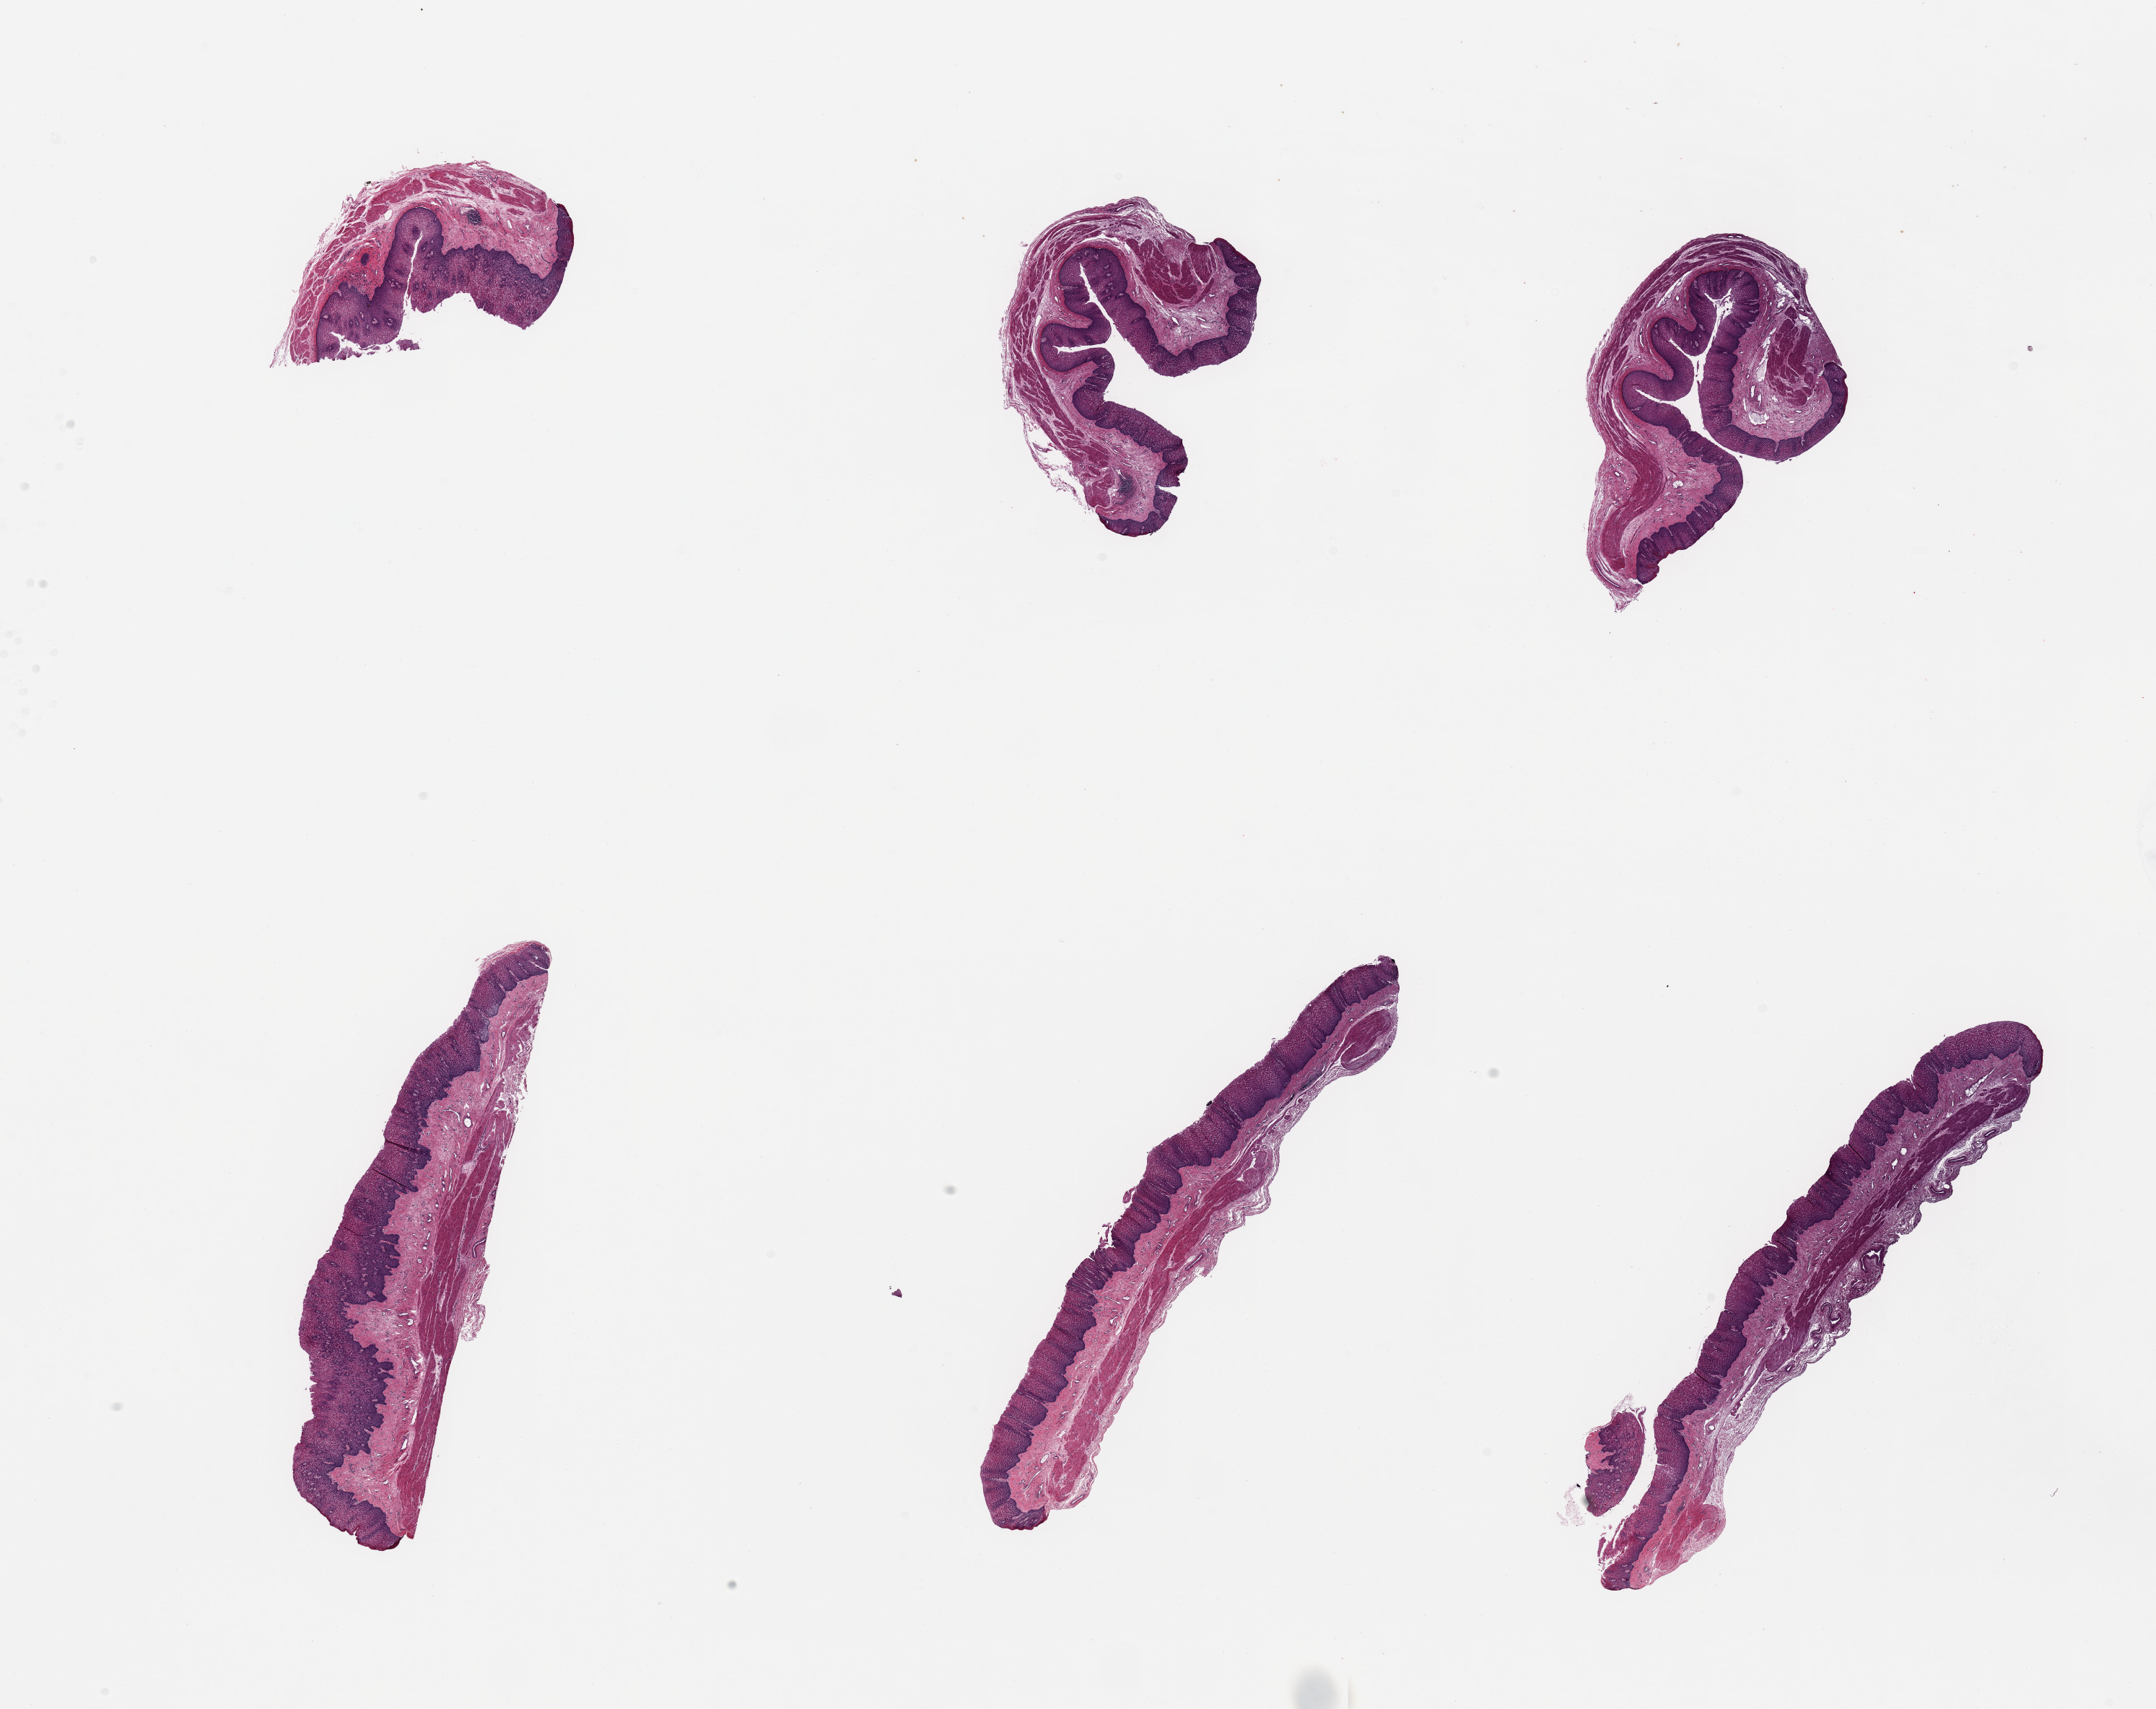
Haematoxylin and eosin whole-slide image — low-resolution overview of the scanned area, about 23.6 x 18.7 mm (from a 20x scan). PAXgene-fixed paraffin-embedded (PFPE) section. Section of esophageal mucous membrane (target tissue). Tissue donor sample. Donor: female.
- review note (as recorded): 6 pieces, squamous mucosa up to ~0.5mm, ~50% thickness